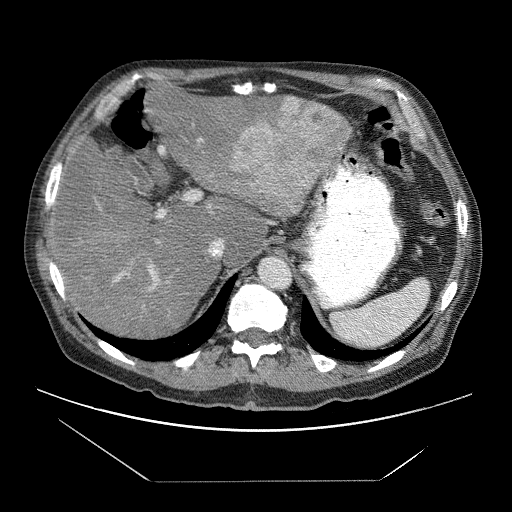
Contrast-enhanced abdominal CT (liver protocol), one axial slice; position 49 of 83 along the scan axis; reconstruction kernel STANDARD; soft-tissue window (W 400 / L 40 HU); 2.5 mm slice thickness; 512 × 512 image matrix, field of view 420 × 420 mm. From the clinical record (not read from this slice): diagnosis: hepatocellular carcinoma (patient treated with transarterial chemoembolisation; whether this scan precedes or follows treatment is not stated here); TNM stage (as recorded): Stage-IVB; Child-Pugh class: B; tumour nodularity: uninodular.
Structures marked on this image (semi-automatic segmentation, software-assisted and operator-edited):
- liver parenchyma outside the tumour (the mass and vessels are separate outlines, so this box may not span the whole liver): bounding box (x1, y1, x2, y2) in pixels: (50, 80, 350, 336)
- mass: (230, 97, 350, 214)
- liver vessels: (113, 138, 212, 291)